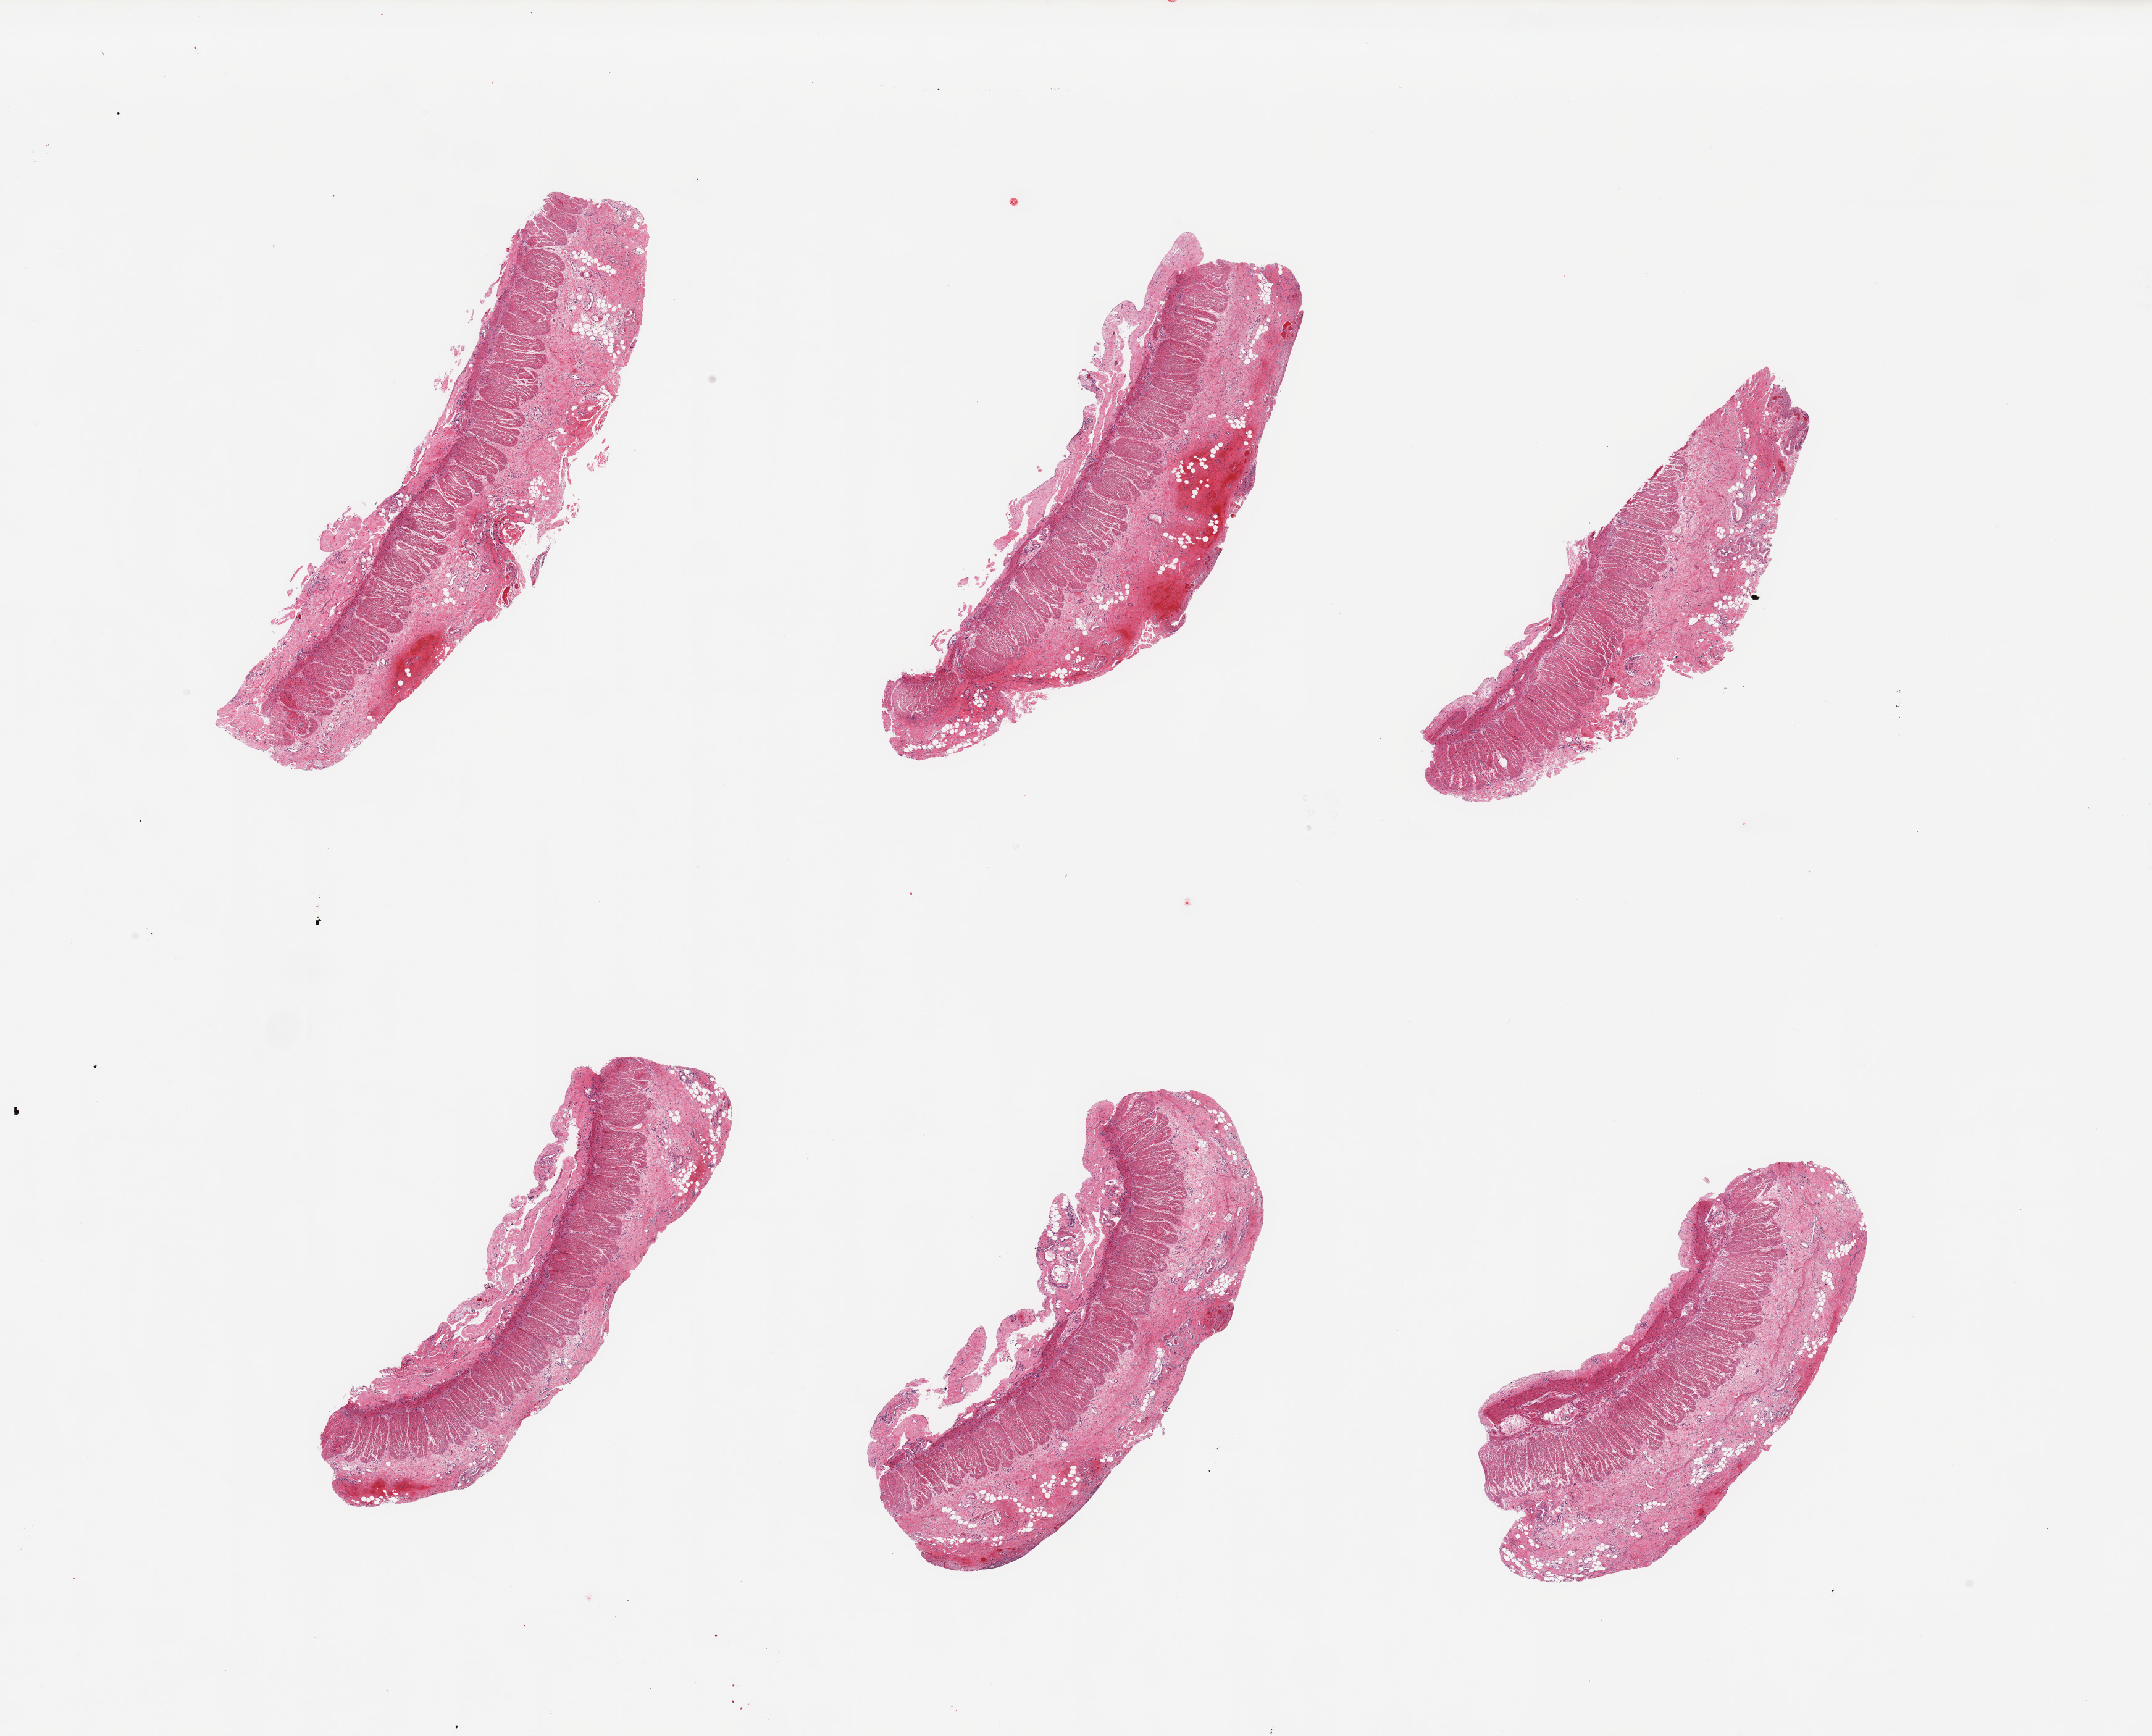
Whole-slide image, hematoxylin and eosin (H&E) stain — low-resolution overview of the scanned area, about 27.6 x 22.2 mm. PAXgene-fixed, paraffin-embedded tissue. Sampled site (target tissue): transverse colon. Donor tissue sample. Donor sex: male.
Review note (as recorded): 6 pieces; submucosa & muscularis propria on all, no mucosa.